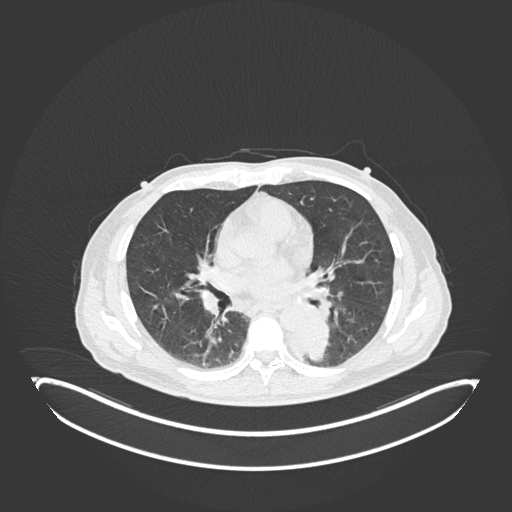
Chest CT, one axial slice. Position 99 of 251 along the scan axis. Reconstruction kernel B30f. 120 kVp. Lung window (W 1500 / L -600 HU). 1 mm slice thickness. 512 × 512 image matrix, field of view 500 × 500 mm. Male patient, age 72 years. From the clinical record (not read from this slice): clinical TNM (as recorded): T2b N0 M1.
Outlined on this slice (bounding box drawn by a radiologist):
- lung tumour (recorded histology: adenocarcinoma): bounding box (x1, y1, x2, y2) in pixels: (283, 319, 333, 364)